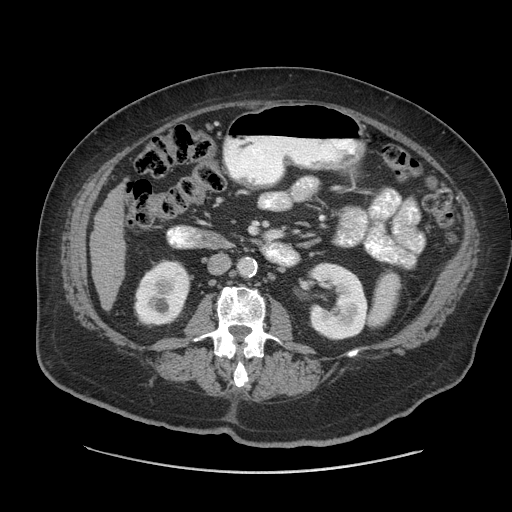
Contrast-enhanced abdominal CT (liver protocol), one axial slice. Slice 16 of 91 in the series (ordered by position). 140 kVp. Soft-tissue window (W 400 / L 40 HU). 512 × 512 image matrix, field of view 420 × 420 mm. From the clinical record (not read from this slice): diagnosis: hepatocellular carcinoma (patient treated with transarterial chemoembolisation; whether this scan precedes or follows treatment is not stated here); TNM stage (as recorded): Stage-I; Child-Pugh class: A.
Annotated regions visible in this slice (semi-automatic segmentation, software-assisted and operator-edited):
- liver parenchyma outside the tumour (the mass and vessels are separate outlines, so this box may not span the whole liver): bounding box [x1, y1, x2, y2] px = [90, 188, 126, 309]